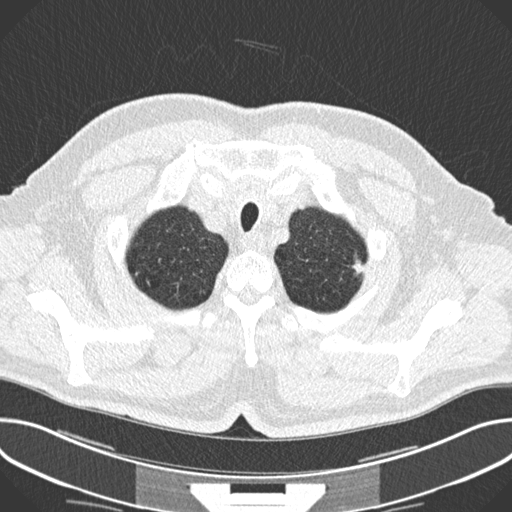
Low-dose screening chest CT, one axial slice. Position 220 of 244 along the scan axis. Lung window (W 1500 / L -600 HU). 2 mm slice thickness. 512 × 512 image matrix, field of view 380 × 380 mm.
Annotated regions visible in this slice (expert manual segmentation):
- lesion 1 (tumor, upper lobe of left lung): bounding box (x1, y1, x2, y2) in pixels: (352, 259, 365, 275)